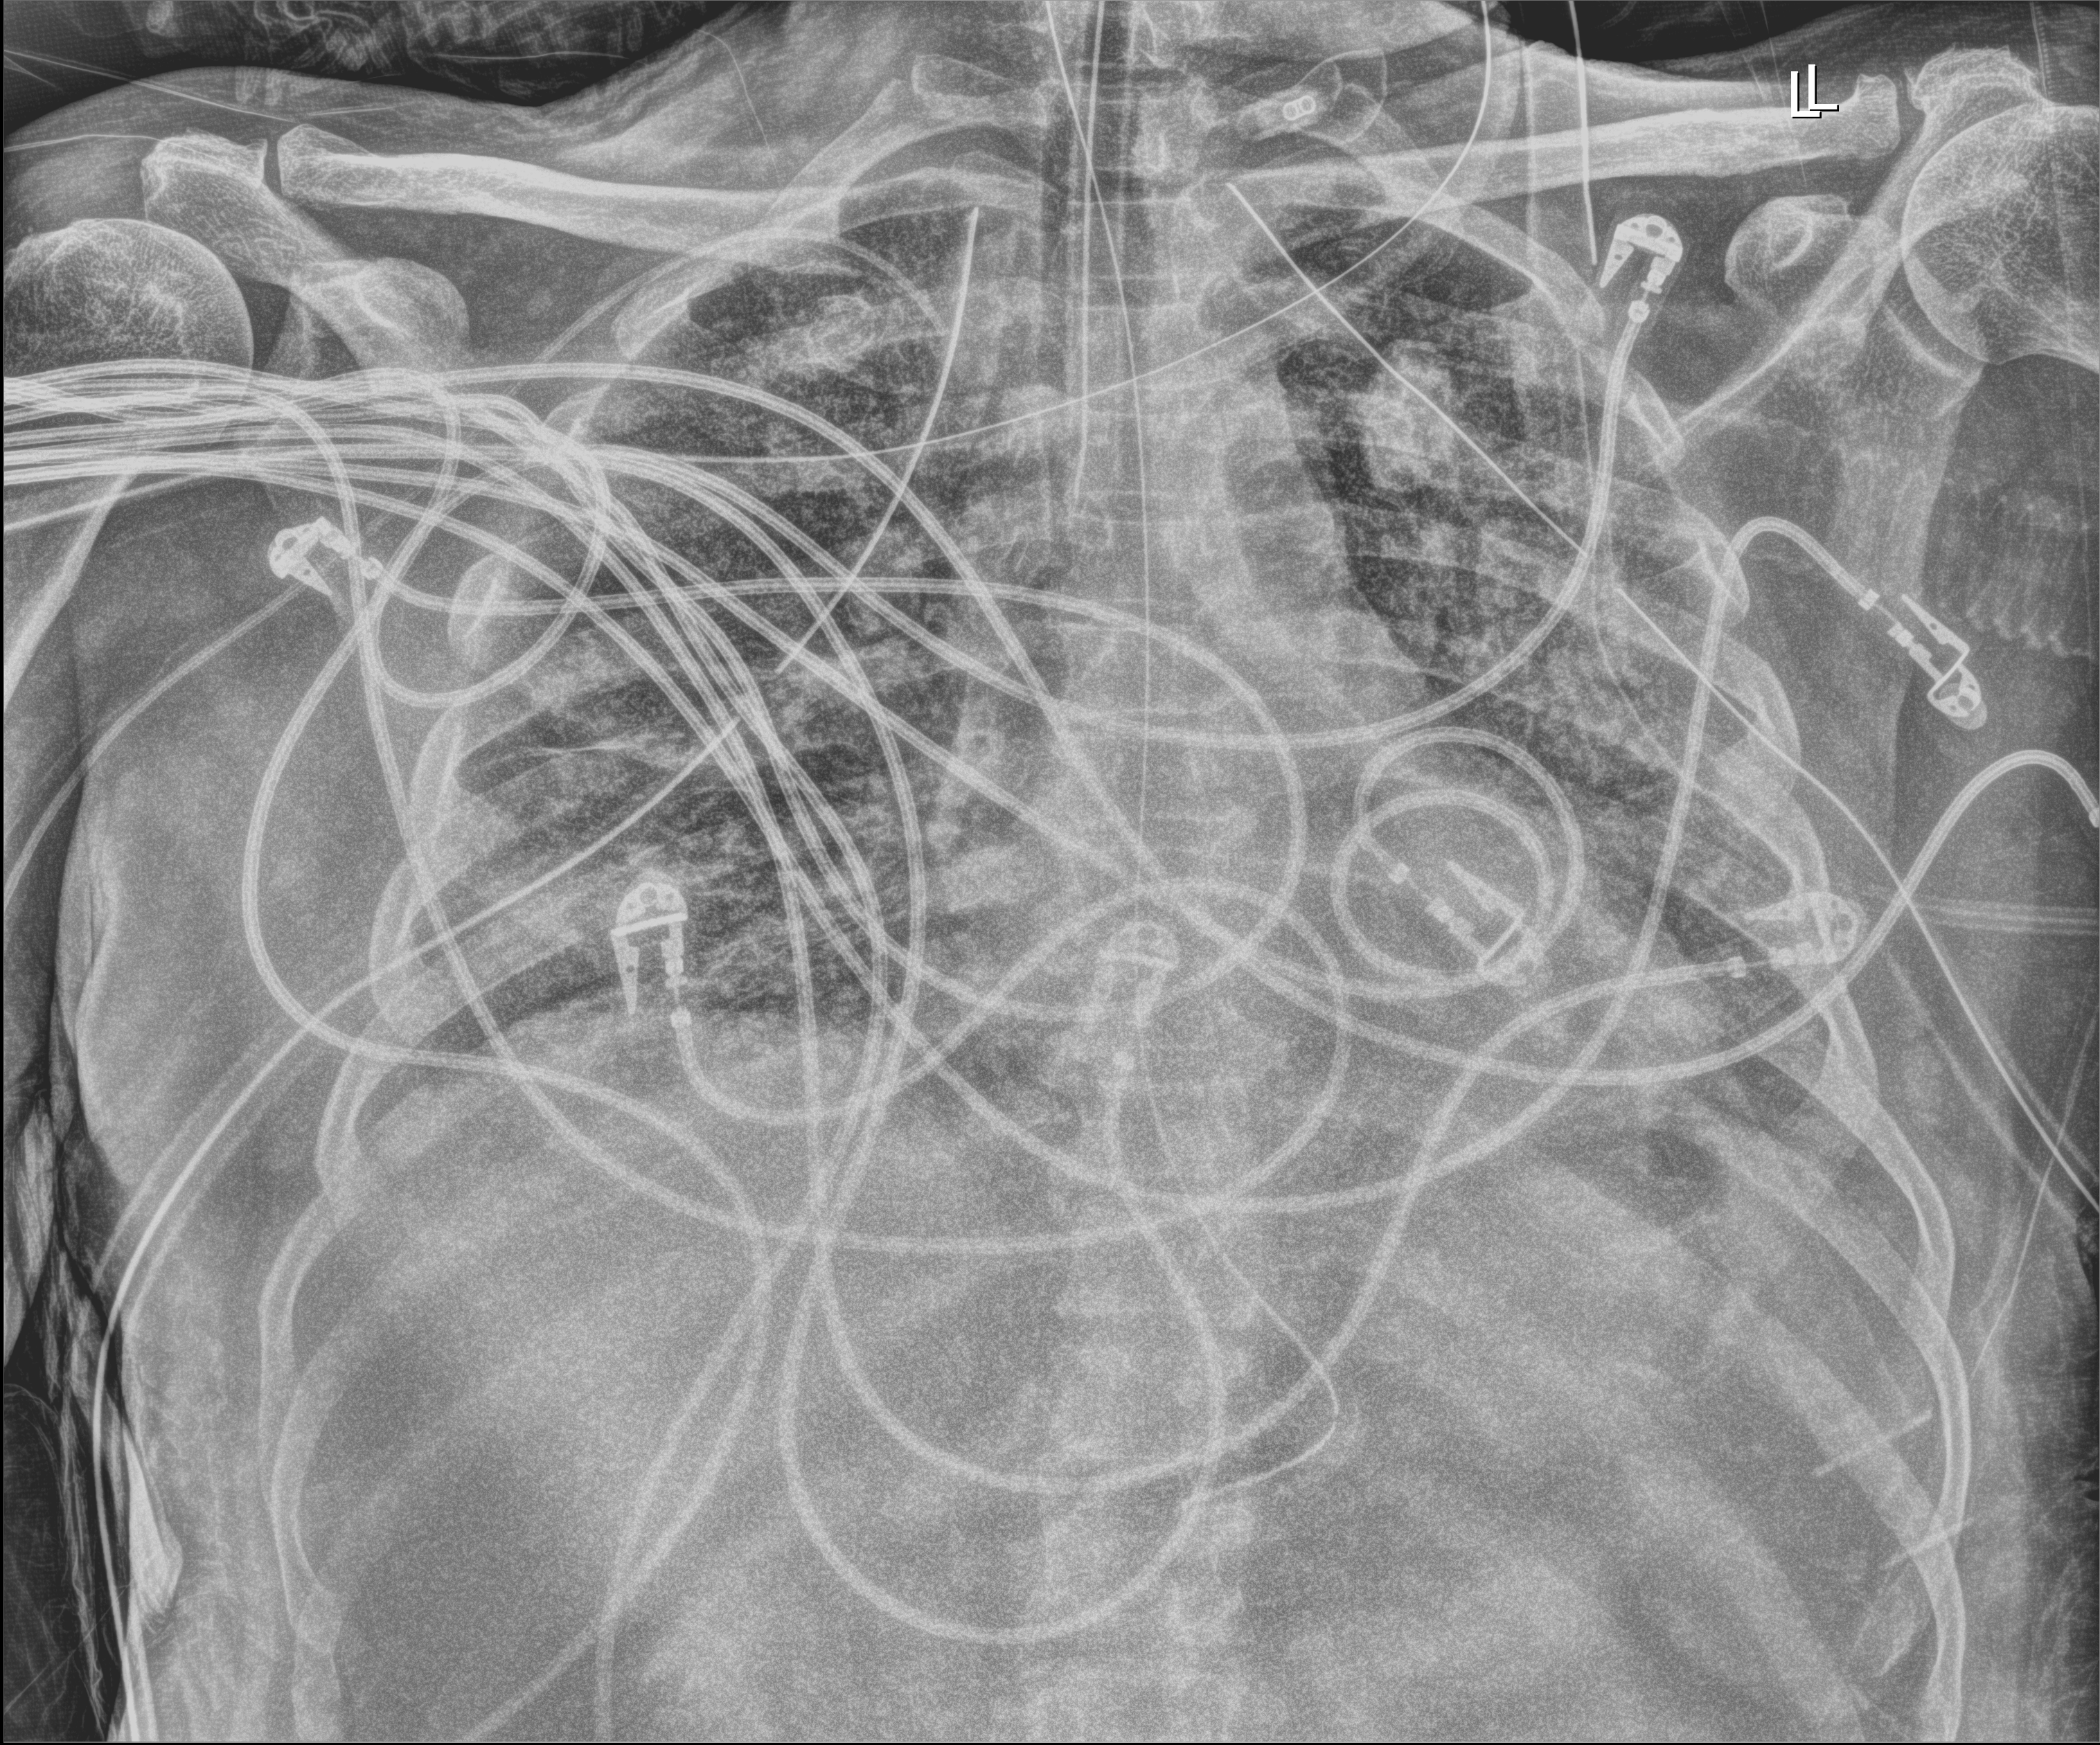
Portable chest radiograph, anteroposterior (AP) projection. Male patient hospitalised with COVID-19, age 18–59 years.
Admission-level facts for this patient (not findings on this image; timing relative to this image not recorded): other chronic lung disease (admission record): no; admitted to intensive care during this hospital stay: yes.